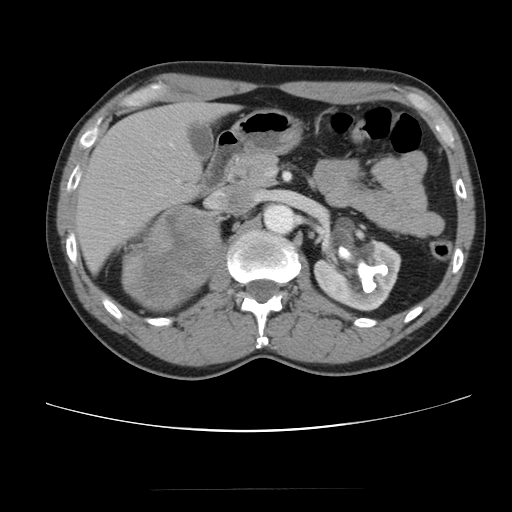
Contrast-enhanced abdominal CT, one axial slice. Position 60 of 80 along the scan axis. Reconstruction kernel STANDARD. Intravenous contrast given. Soft-tissue window (W 400 / L 40 HU). 512 × 512 image matrix, field of view 360 × 360 mm. Male patient, age 61 years. From the clinical record (not read from this slice): diagnosis: adrenocortical carcinoma; tumour side: right adrenal; tumour size at pathology: 11.1 cm; Ki-67 index: 32 %; stage (as recorded): 2.
Annotated regions visible in this slice (semi-automatic segmentation, software-assisted and operator-edited):
- mass: bounding box (x1, y1, x2, y2) in pixels: (123, 207, 220, 309)